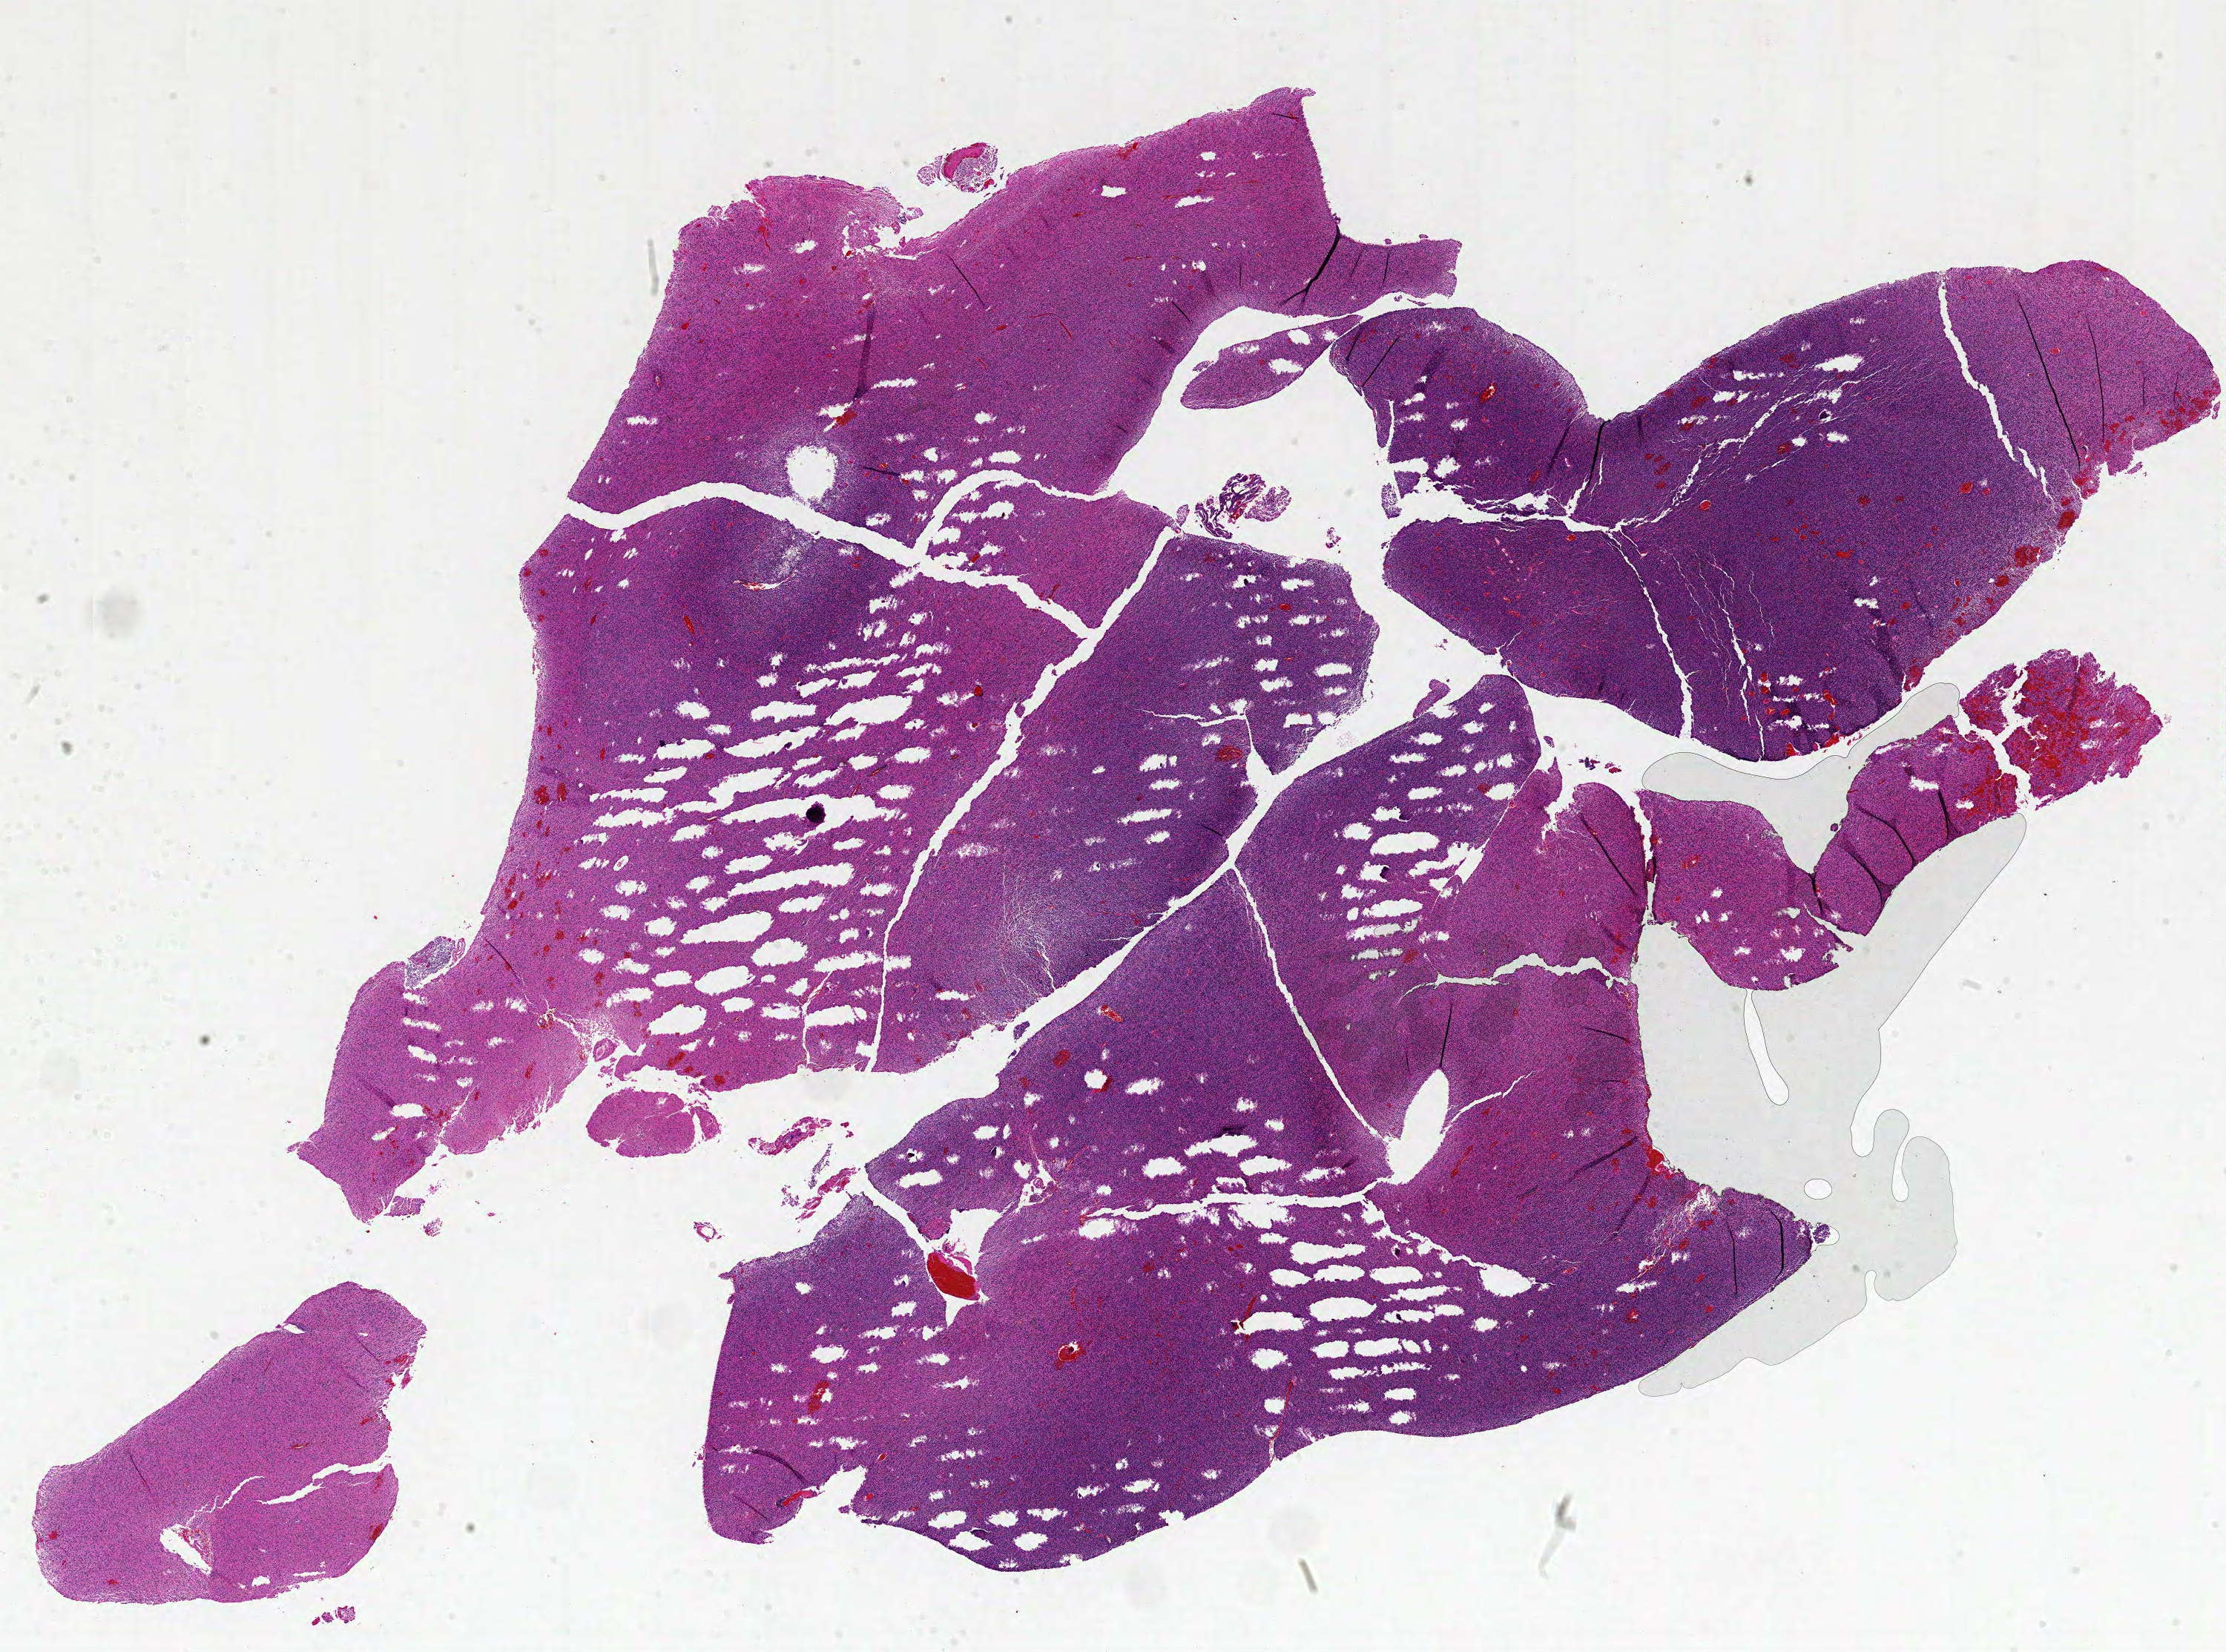
H&E whole-slide image — a low-resolution overview of the entire scanned area, about 24.0 x 17.8 mm. Formalin-fixed paraffin-embedded (FFPE) diagnostic section. Sample: primary tumour, brain. Patient: male, age at initial diagnosis 46 years.
Pathologic diagnosis: Glioblastoma.